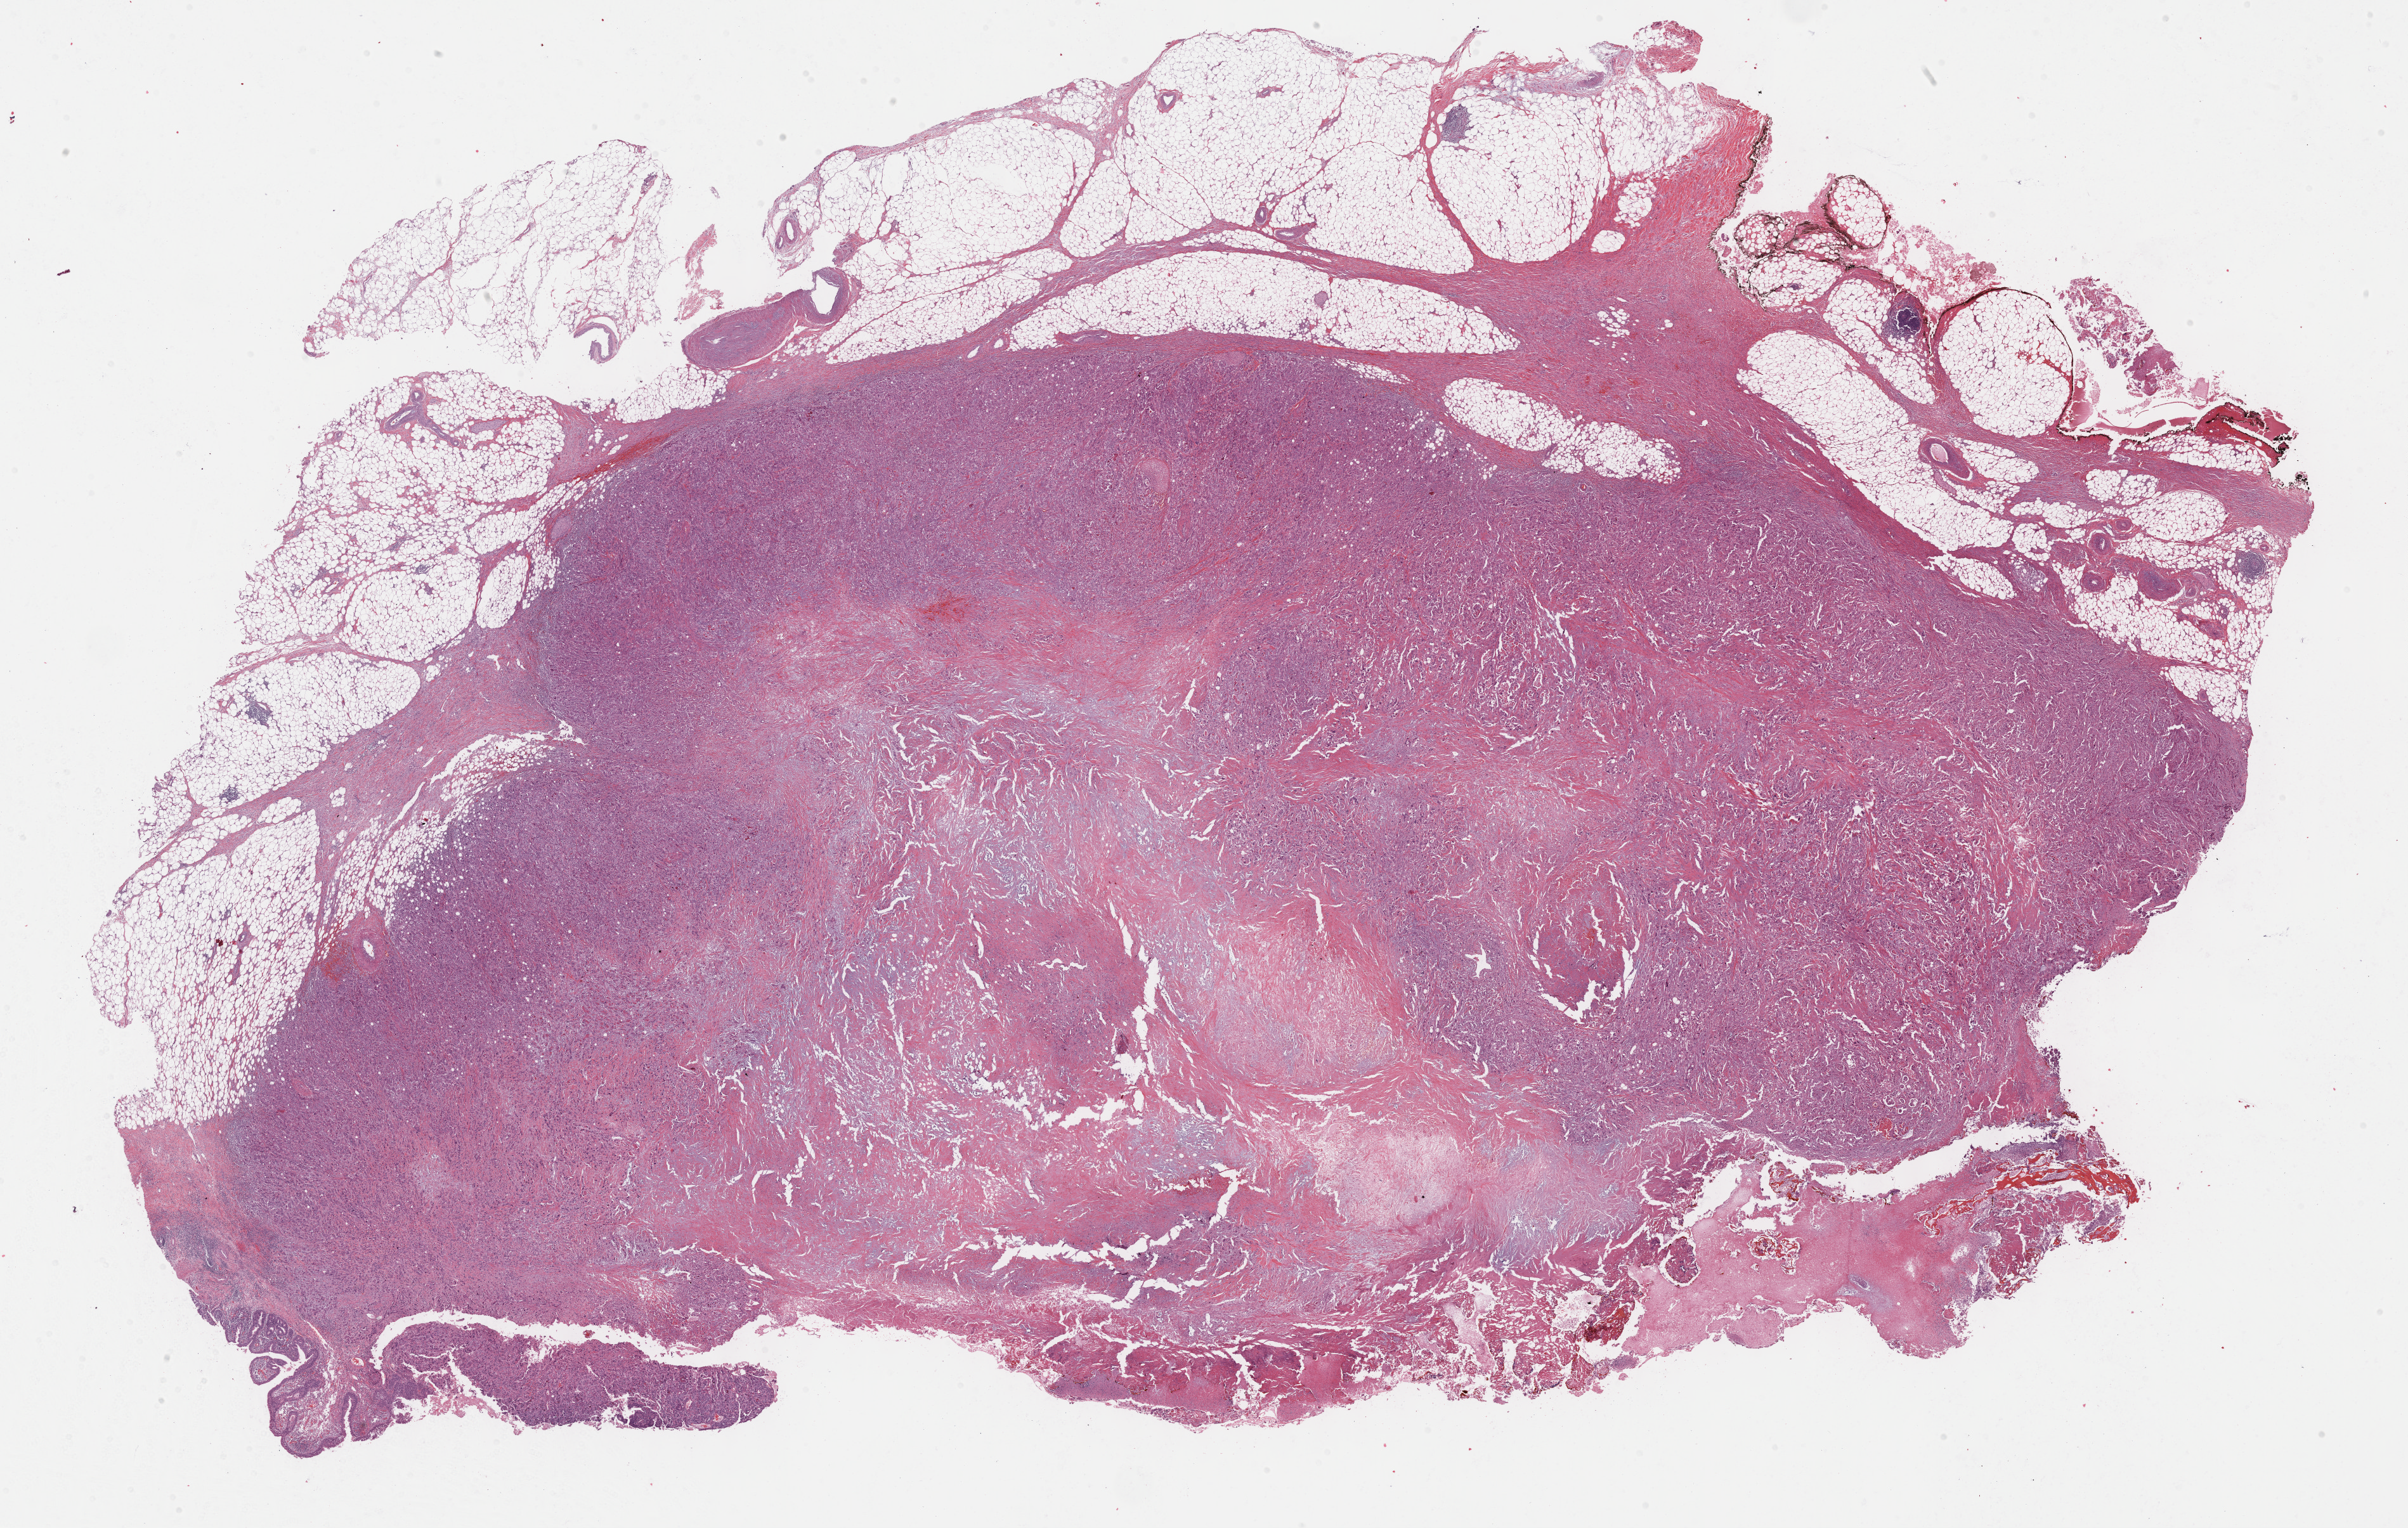
H&E-stained whole-slide image — a low-resolution overview of the entire scanned area, about 30.7 x 19.5 mm (acquisition: 40x scan), formalin-fixed paraffin-embedded (FFPE) diagnostic section, bladder, primary tumour sample. Patient: male, age at initial diagnosis 83 years. Histologic grade: high grade.
Lymph nodes positive (case pathology): 16 of 64 examined. Pathologic diagnosis: Transitional cell carcinoma. AJCC pathologic stage: IV (6th edition).